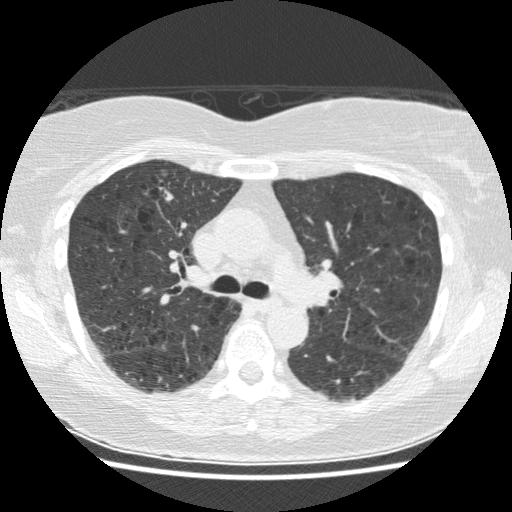
Chest CT (low-dose screening protocol), one axial image, baseline annual screen, lung window (W 1500 / L -600 HU), 2.5 mm slice thickness. Female, age 63 years at enrolment. Current smoker at enrolment.
Expert-annotated lung lesion, bounding box [x1, y1, x2, y2] px = [142, 158, 182, 208]. Reader record for this screening exam (exam-level; its link to the box is not recorded): non-calcified nodule or mass ≥4 mm, right upper lobe, 18 × 14 mm, spiculated (stellate) margins, soft tissue attenuation. Official screen result: positive, change unspecified: nodule(s) >= 4 mm or enlarging nodule(s), mass(es), or other non-specific abnormalities suspicious for lung cancer. Lung cancer was diagnosed 87 days after this screen: papillary adenocarcinoma, NOS, right upper lobe, well differentiated (G1), stage IA (AJCC 6th edition), 19 mm at pathology.